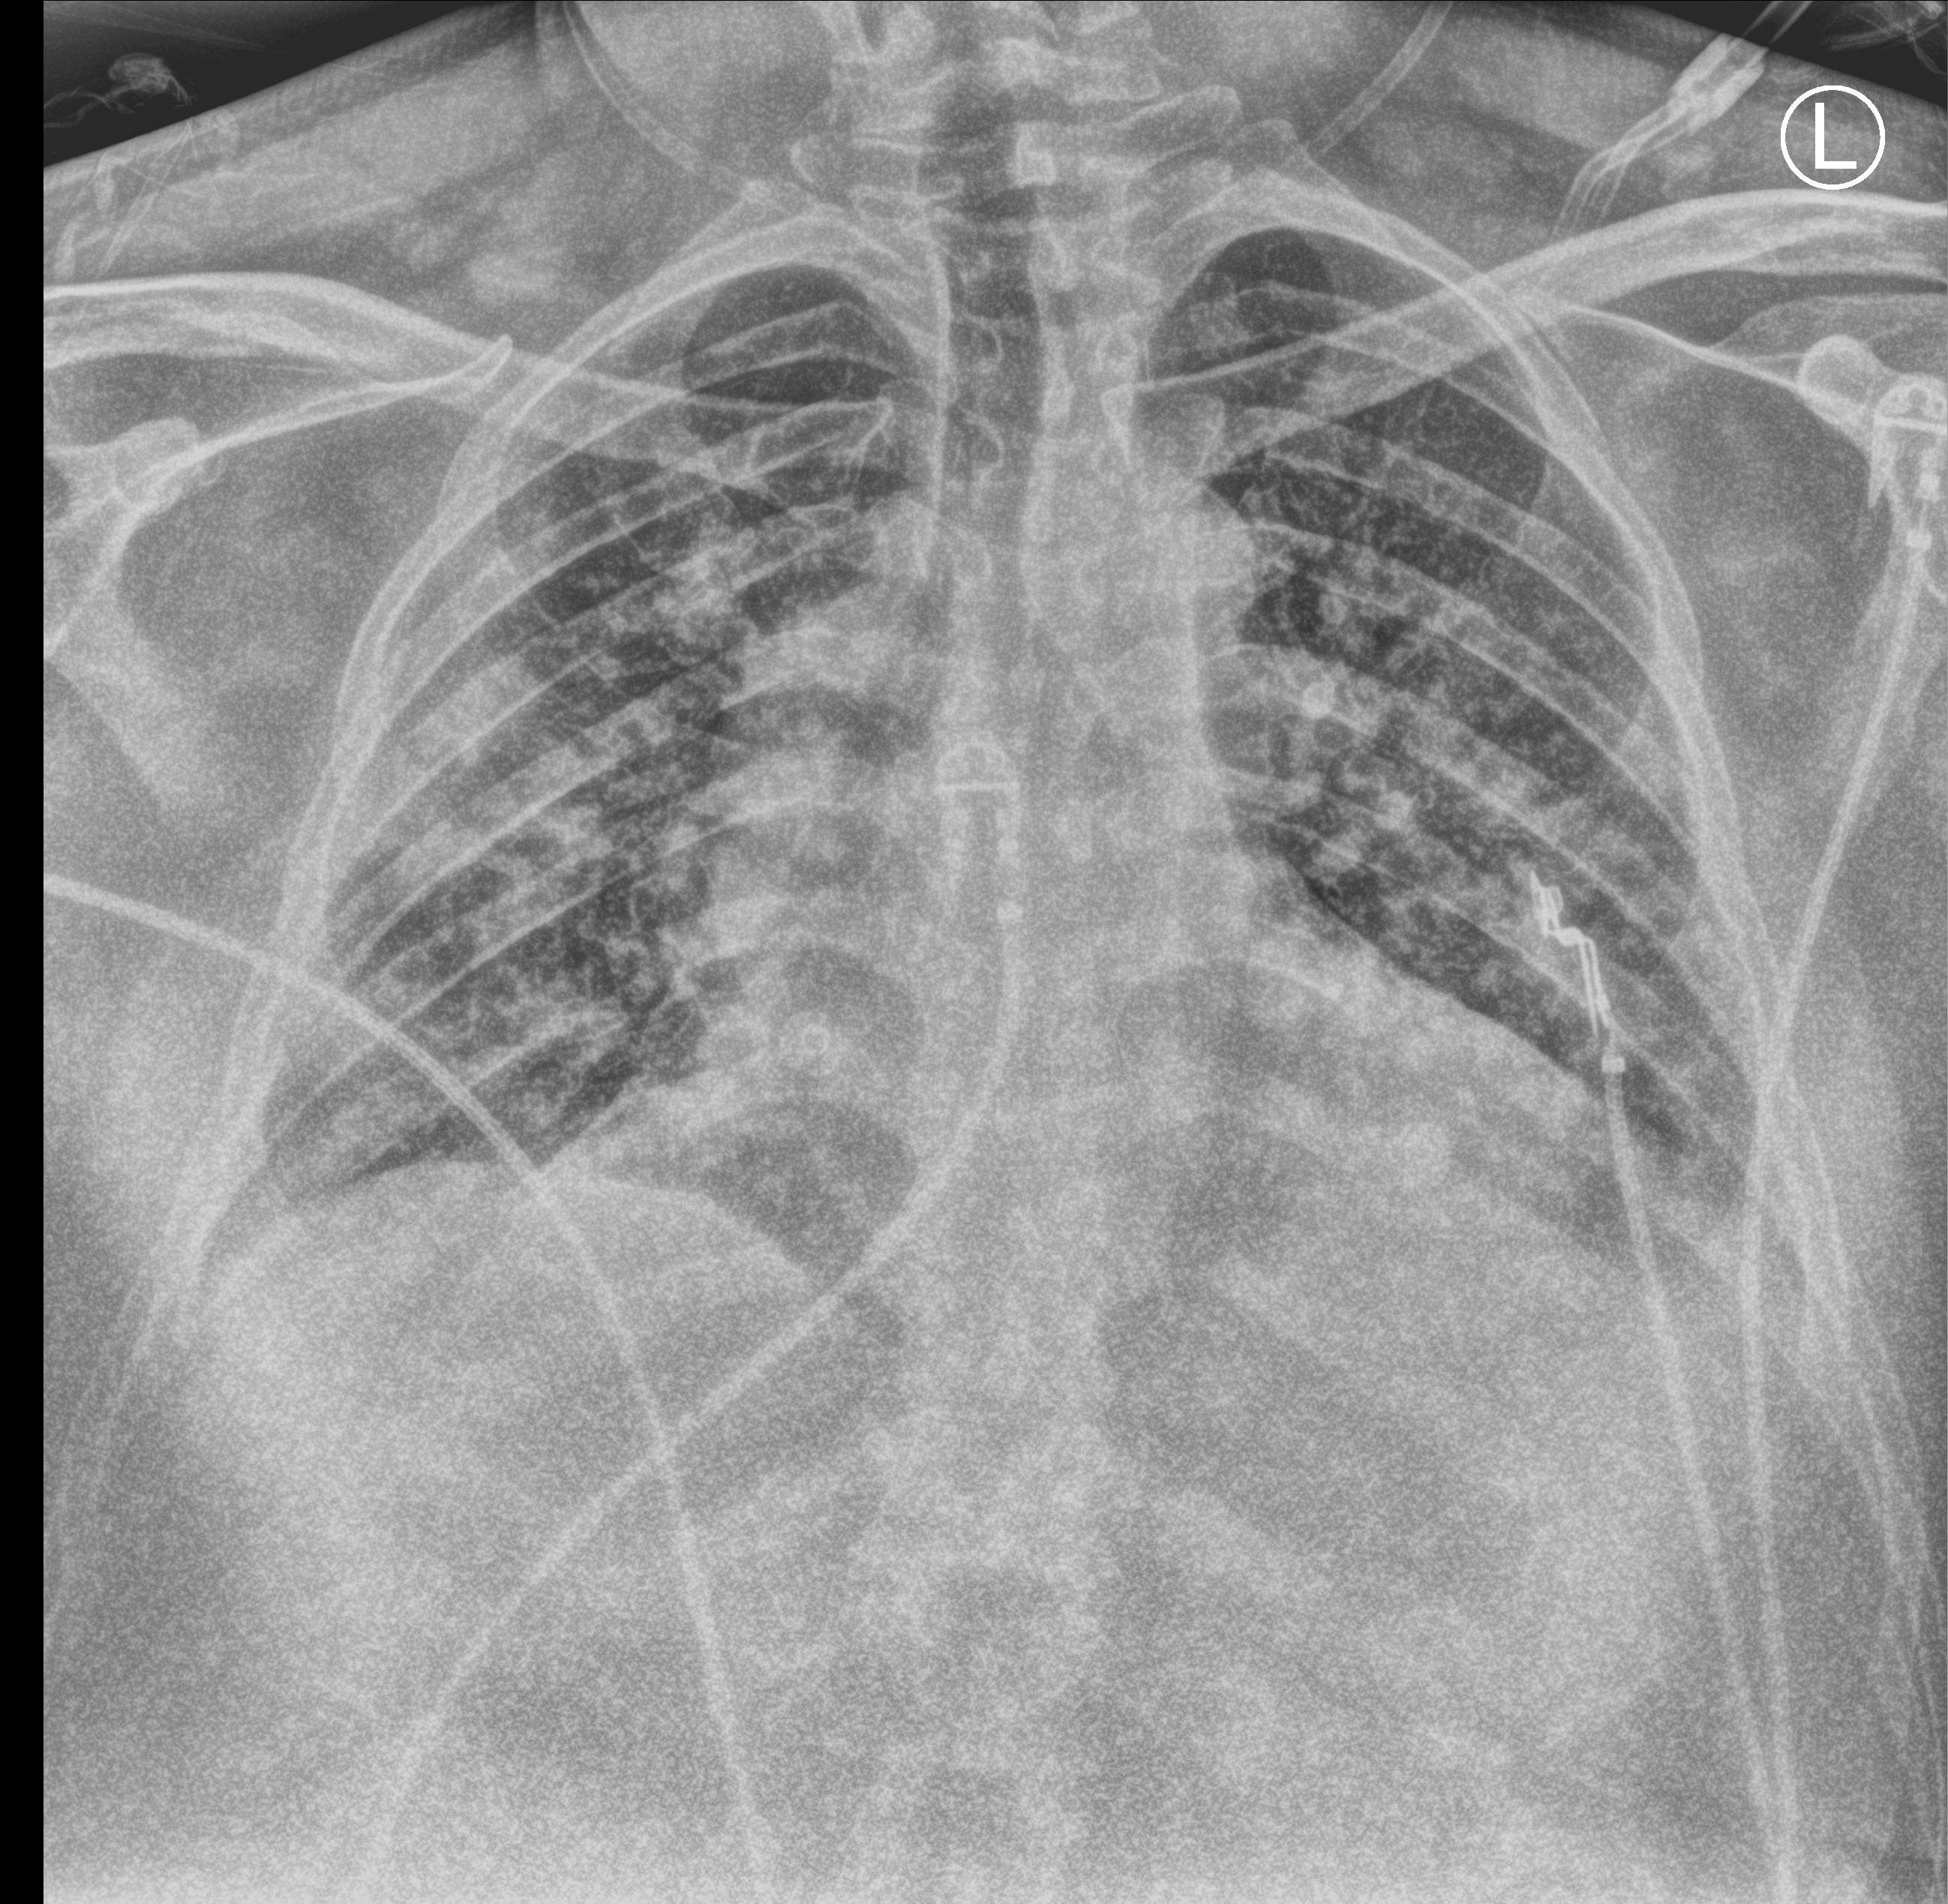
Portable chest radiograph, anteroposterior (AP) projection. Male patient hospitalised with COVID-19, age 18–59 years.
Hospital-stay facts (about this admission, not read from this image; timing relative to this image not recorded):
- admitted to intensive care during this hospital stay: yes
- mechanically ventilated during this hospital stay: yes